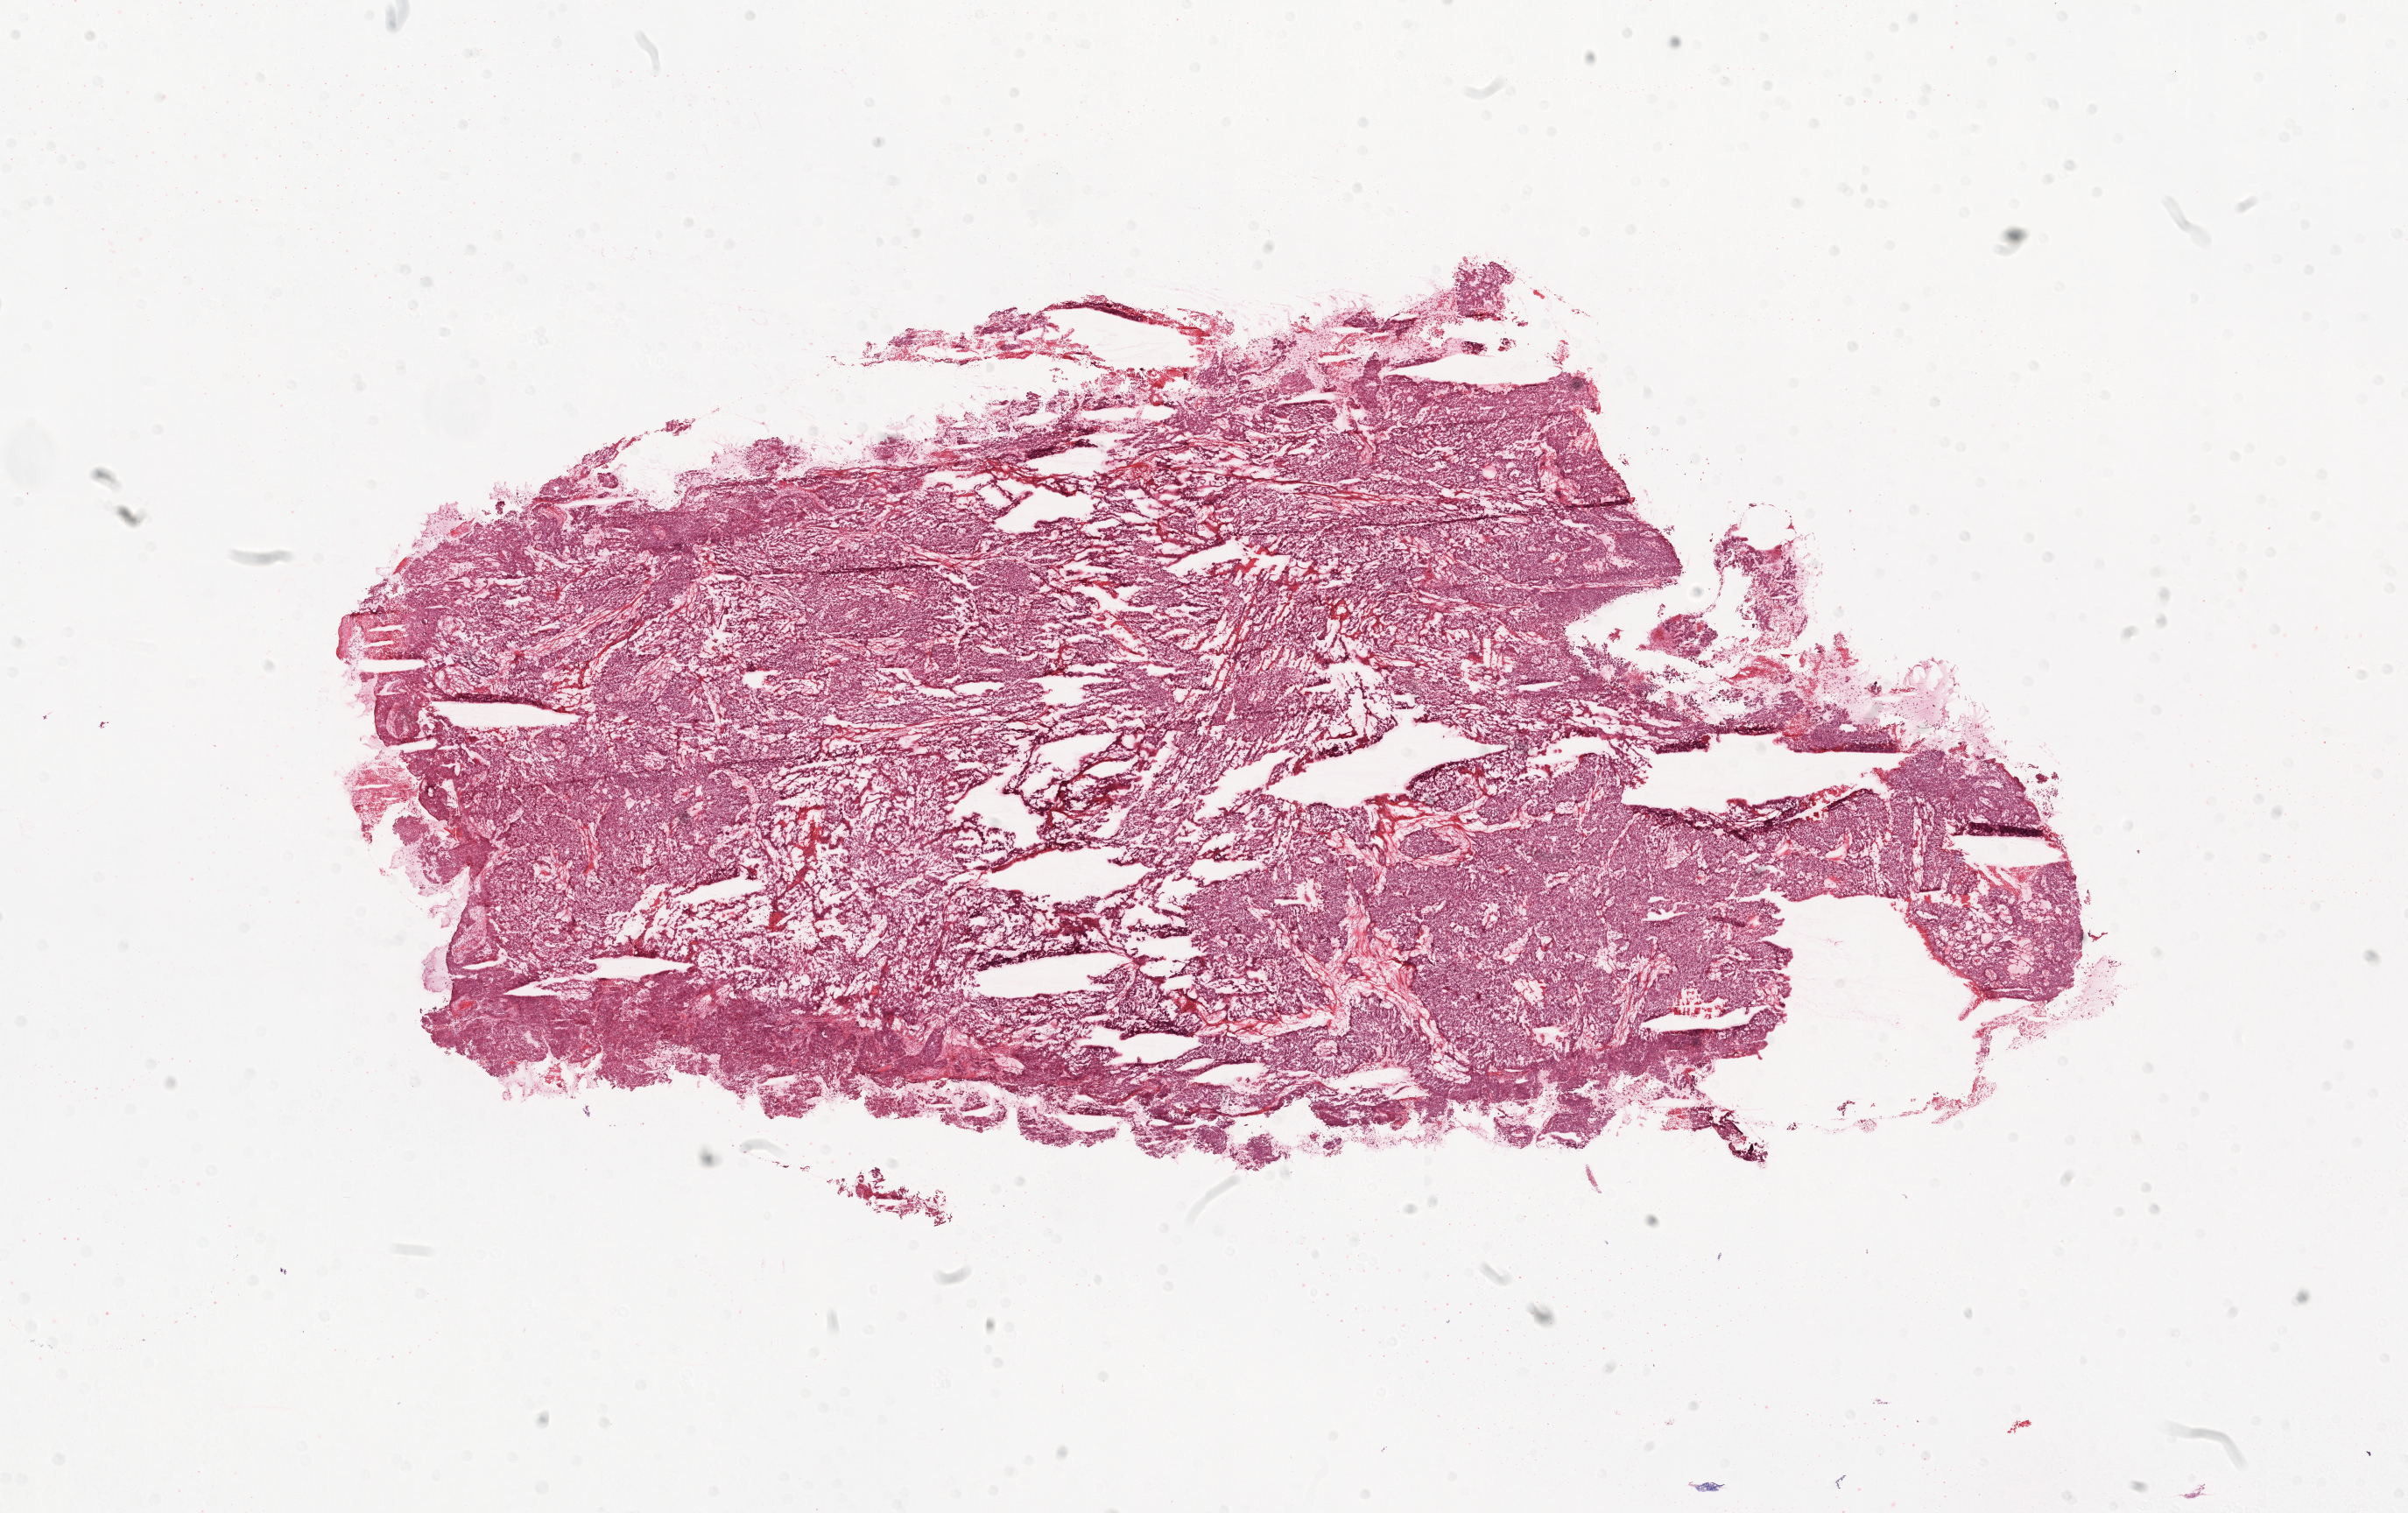
Whole-slide histology image, Hematoxylin and eosin (H&E) stained — a low-resolution overview of the entire scanned area, about 22.1 x 13.9 mm. Frozen section from the top of the tissue portion. Sample: primary tumour, ovary. Patient: female, age at initial diagnosis 40 years. Histologic grade: G3 (poorly differentiated). Slide review estimates, as recorded: tumour cells 75%, tumour nuclei 95%, normal cells 13%, stromal cells 5%, necrosis 7%.
• FIGO stage: IIIC
• pathologic diagnosis: Serous cystadenocarcinoma, NOS
• laterality: bilateral